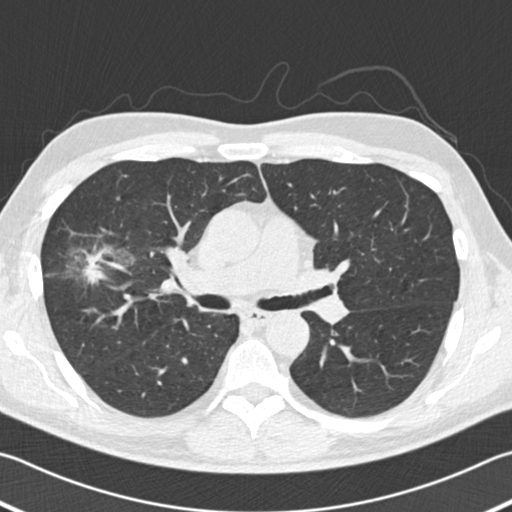
Low-dose screening chest CT, one axial slice; slice 114 of 182 in the series (ordered by position); reconstruction kernel B30f; 120 kVp; lung window (W 1500 / L -600 HU); 2 mm slice thickness; 512 × 512 image matrix.
Outlined on this slice (outlined manually by an expert reader):
- lesion 1 (tumor, upper lobe of right lung): bounding box <68,245,135,283> (left, top, right, bottom; pixels)